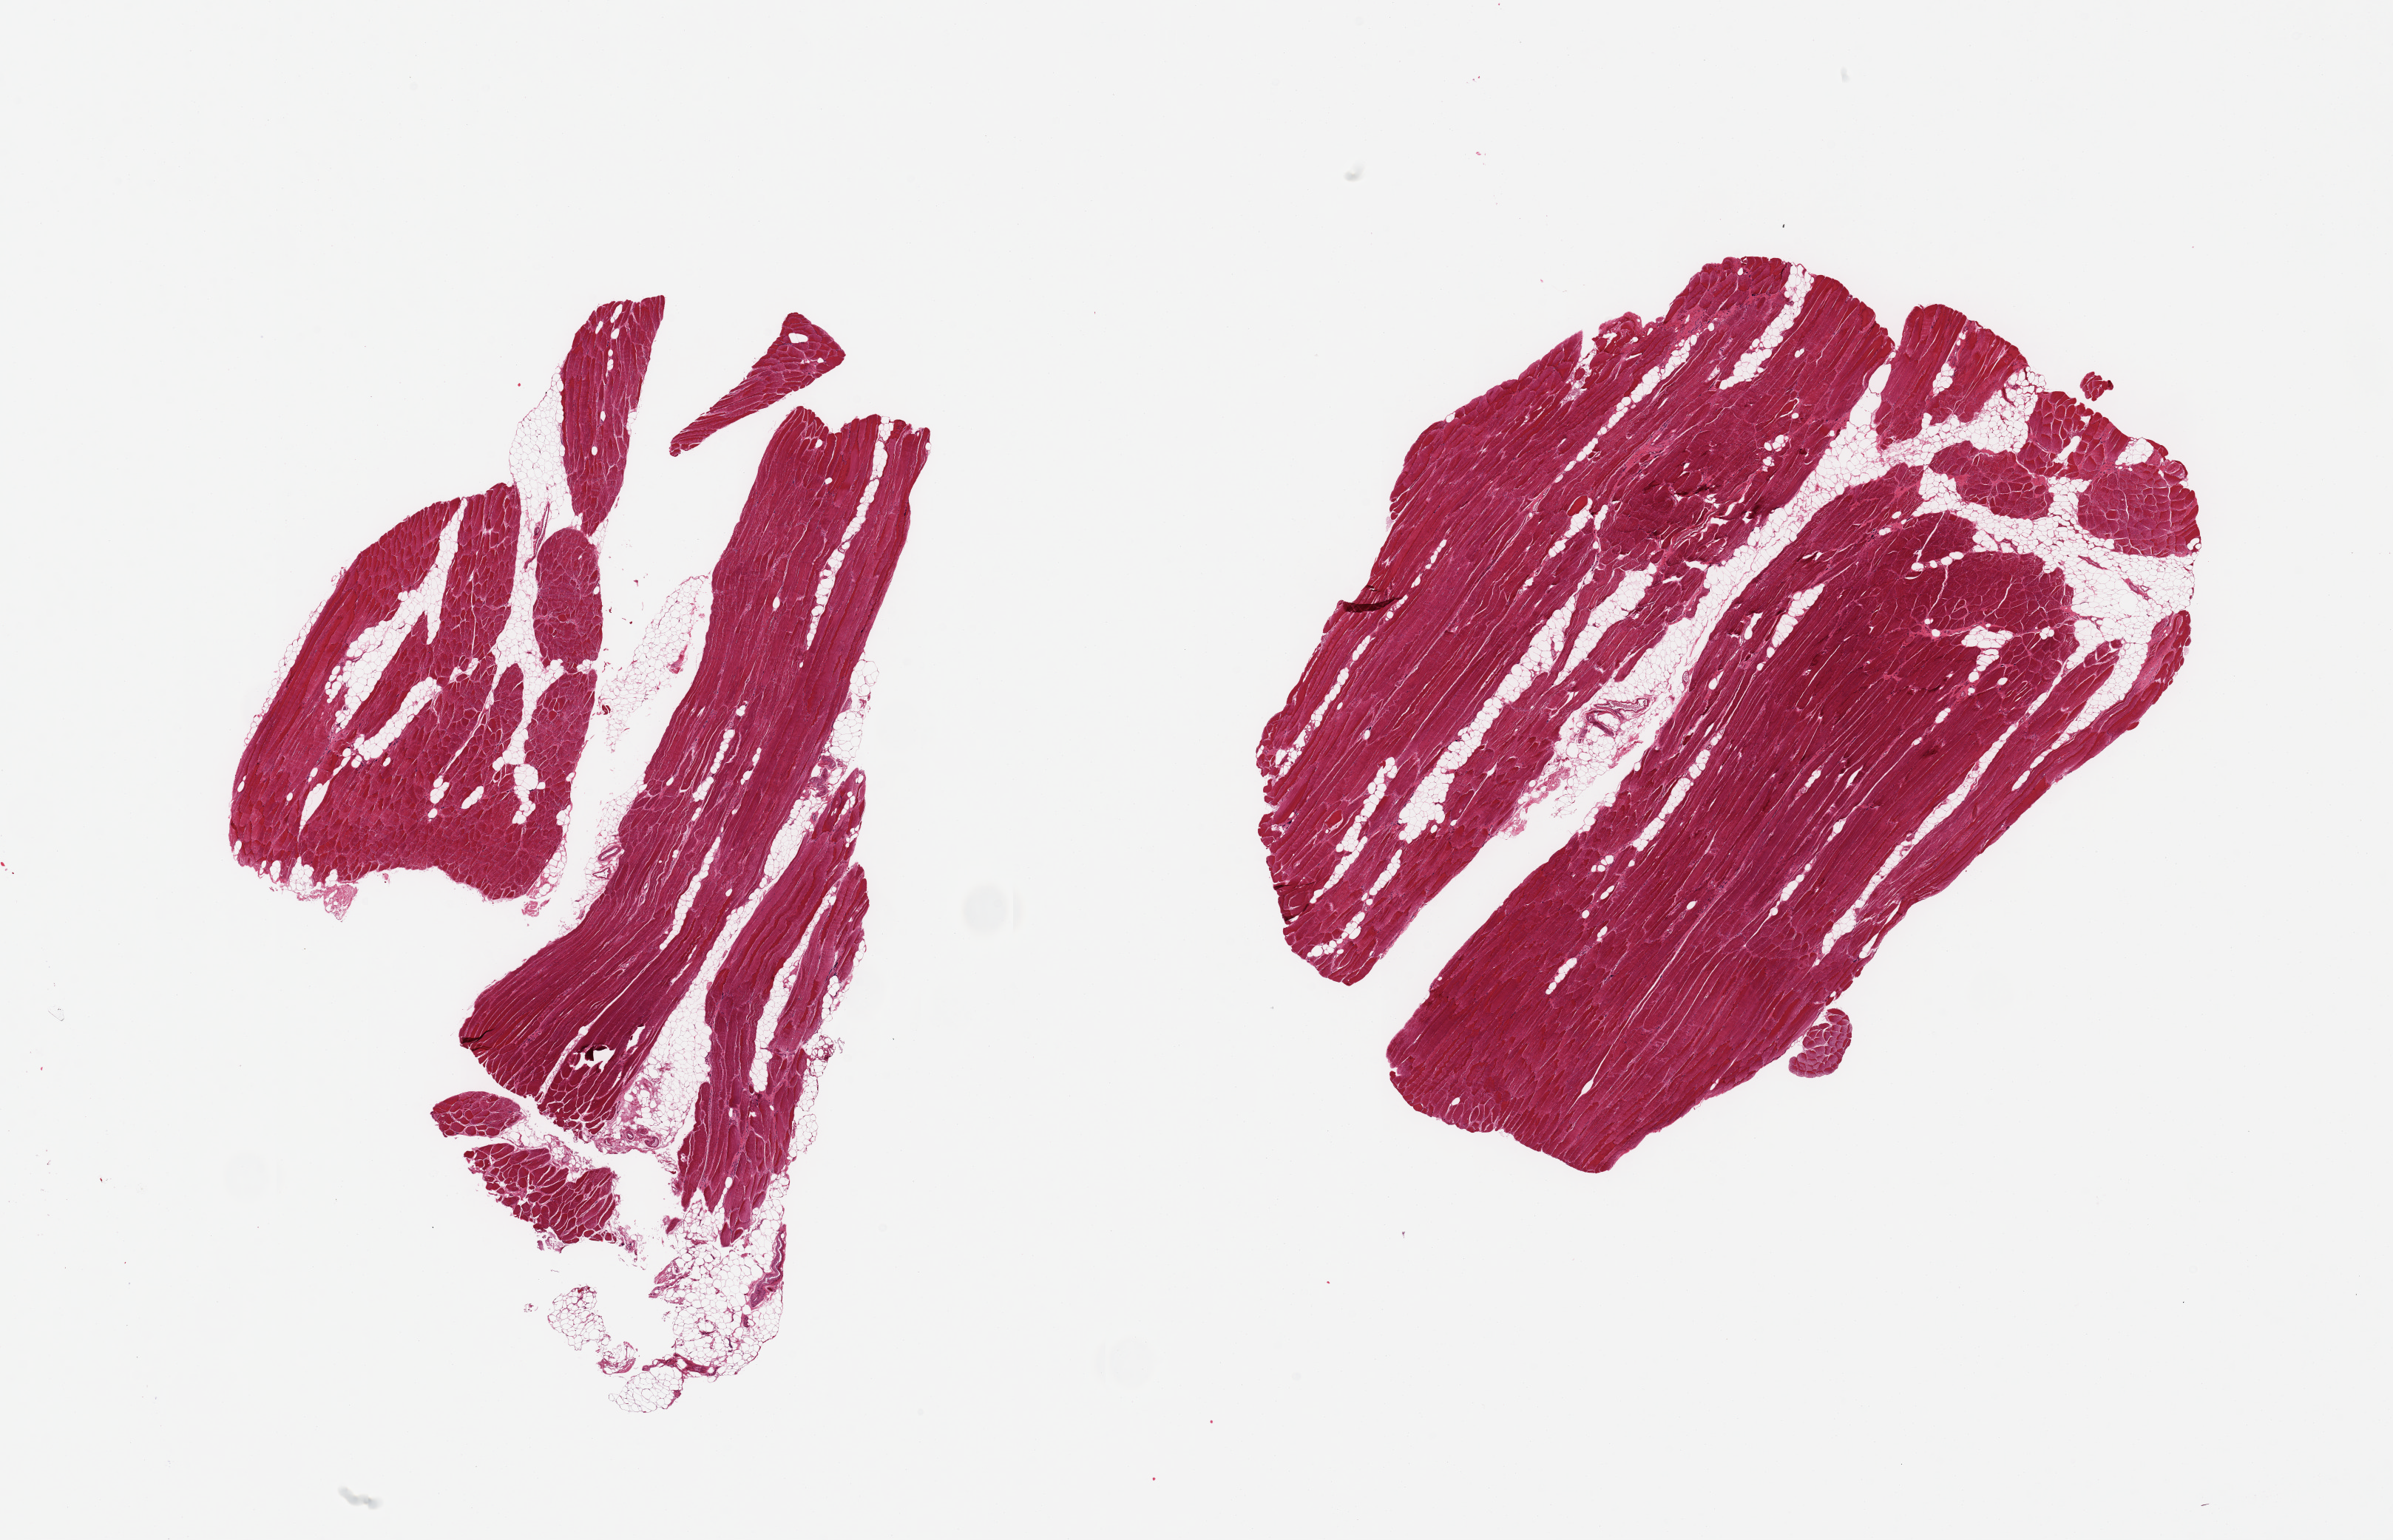
Digitized hematoxylin and eosin (H&E)-stained section, brightfield — whole scanned area (about 25.6 x 16.5 mm) shown as a low-resolution overview. PAXgene-fixed, paraffin-embedded tissue. Sampled site (target tissue): skeletal muscle. Donor tissue sample.
Pathologist's review note for this sample: 2 pieces, 10-15% interstitial fat.